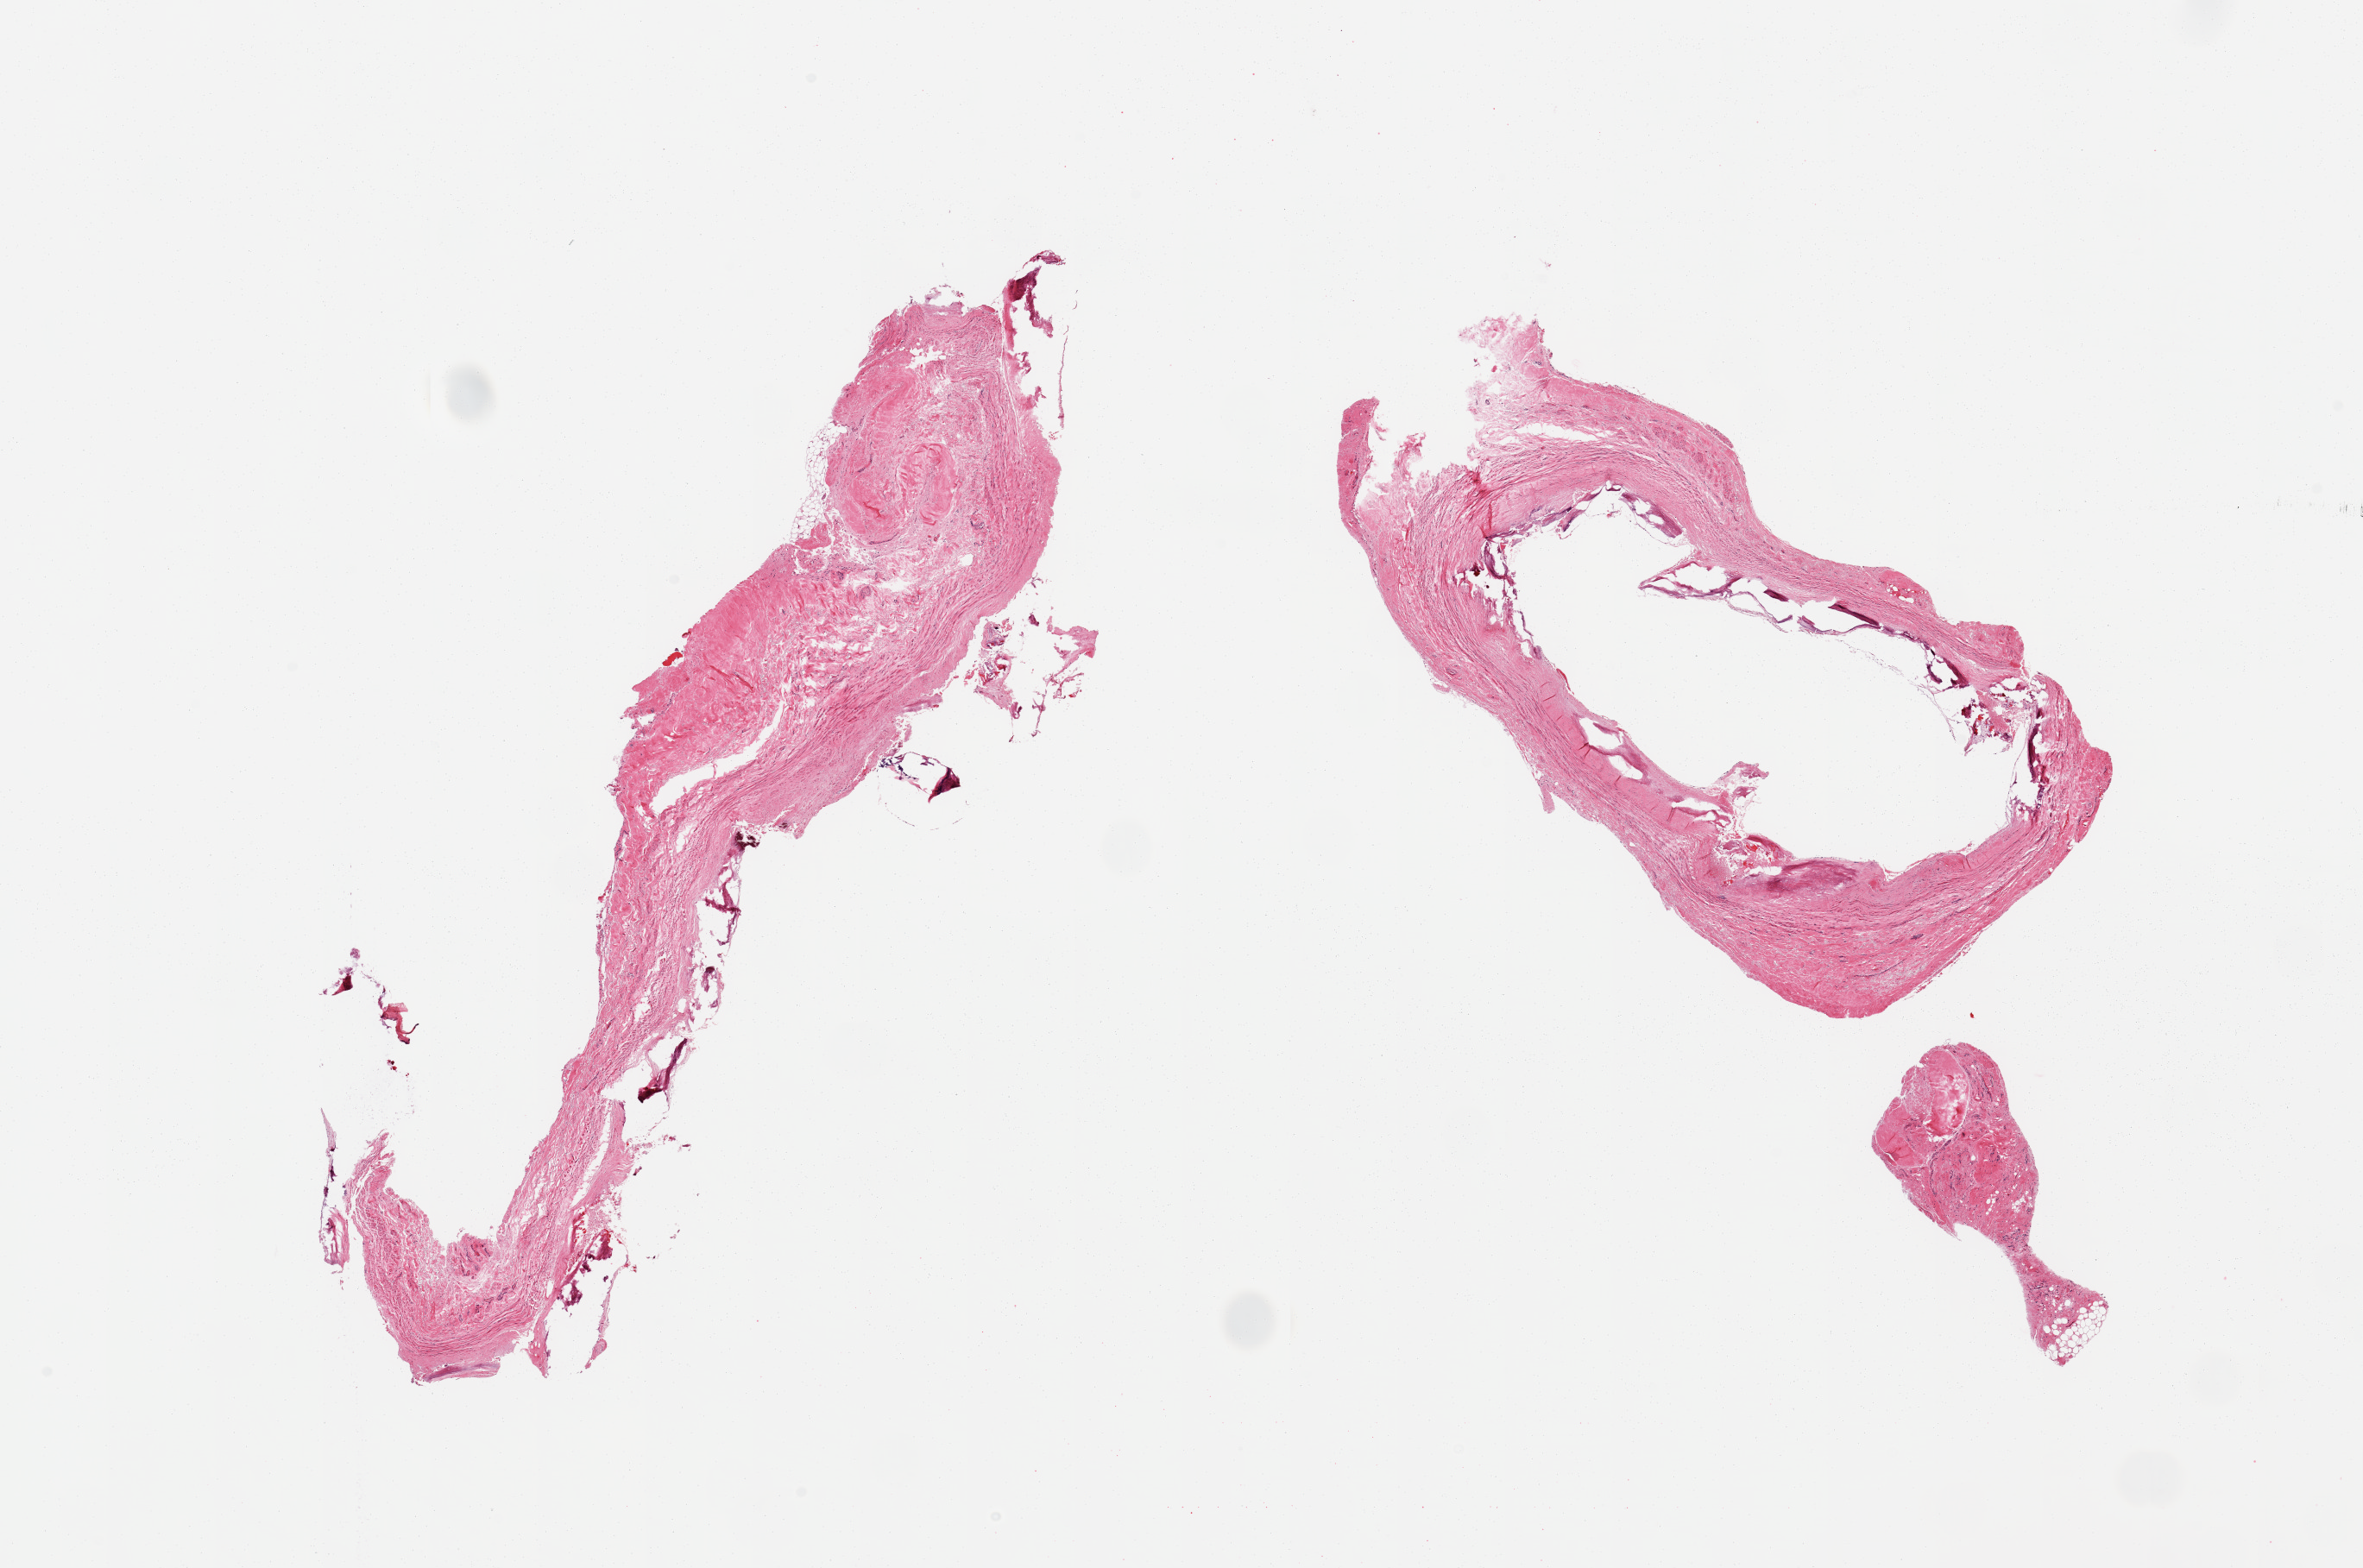
Digitized H&E-stained section, low-resolution overview of the scanned area, about 21.7 x 14.4 mm; PAXgene-fixed, paraffin-embedded tissue; target tissue: coronary artery; tissue donor sample. Male donor.
Reviewer comment on this tissue sample: 2 pieces, fragmented, calcified atherosis, partially occlusive.